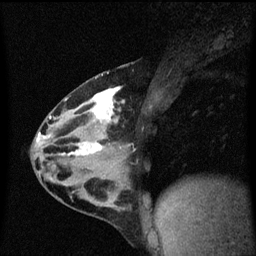
Breast MRI (dynamic contrast-enhanced), one sagittal slice. Position 31 of 60 along the scan axis. Dynamic contrast-enhanced series, image 2 of 3 at this slice position (ordered by acquisition). 1.5 T. TE 4.2 ms, TR 8.4 ms. 256 × 256 image matrix, field of view 200 × 200 mm. Female patient, age 32 years.
Structures marked on this image (semi-automatic segmentation, software-assisted and operator-edited):
- analysis volume of interest (the breast-tissue region the enhancement analysis was run in; not a lesion): bounding box (x1, y1, x2, y2) in pixels: (34, 74, 150, 169)
- tumour enhancement mask (voxels above the 70 % enhancement threshold inside the analysis volume of interest): (38, 88, 125, 157)